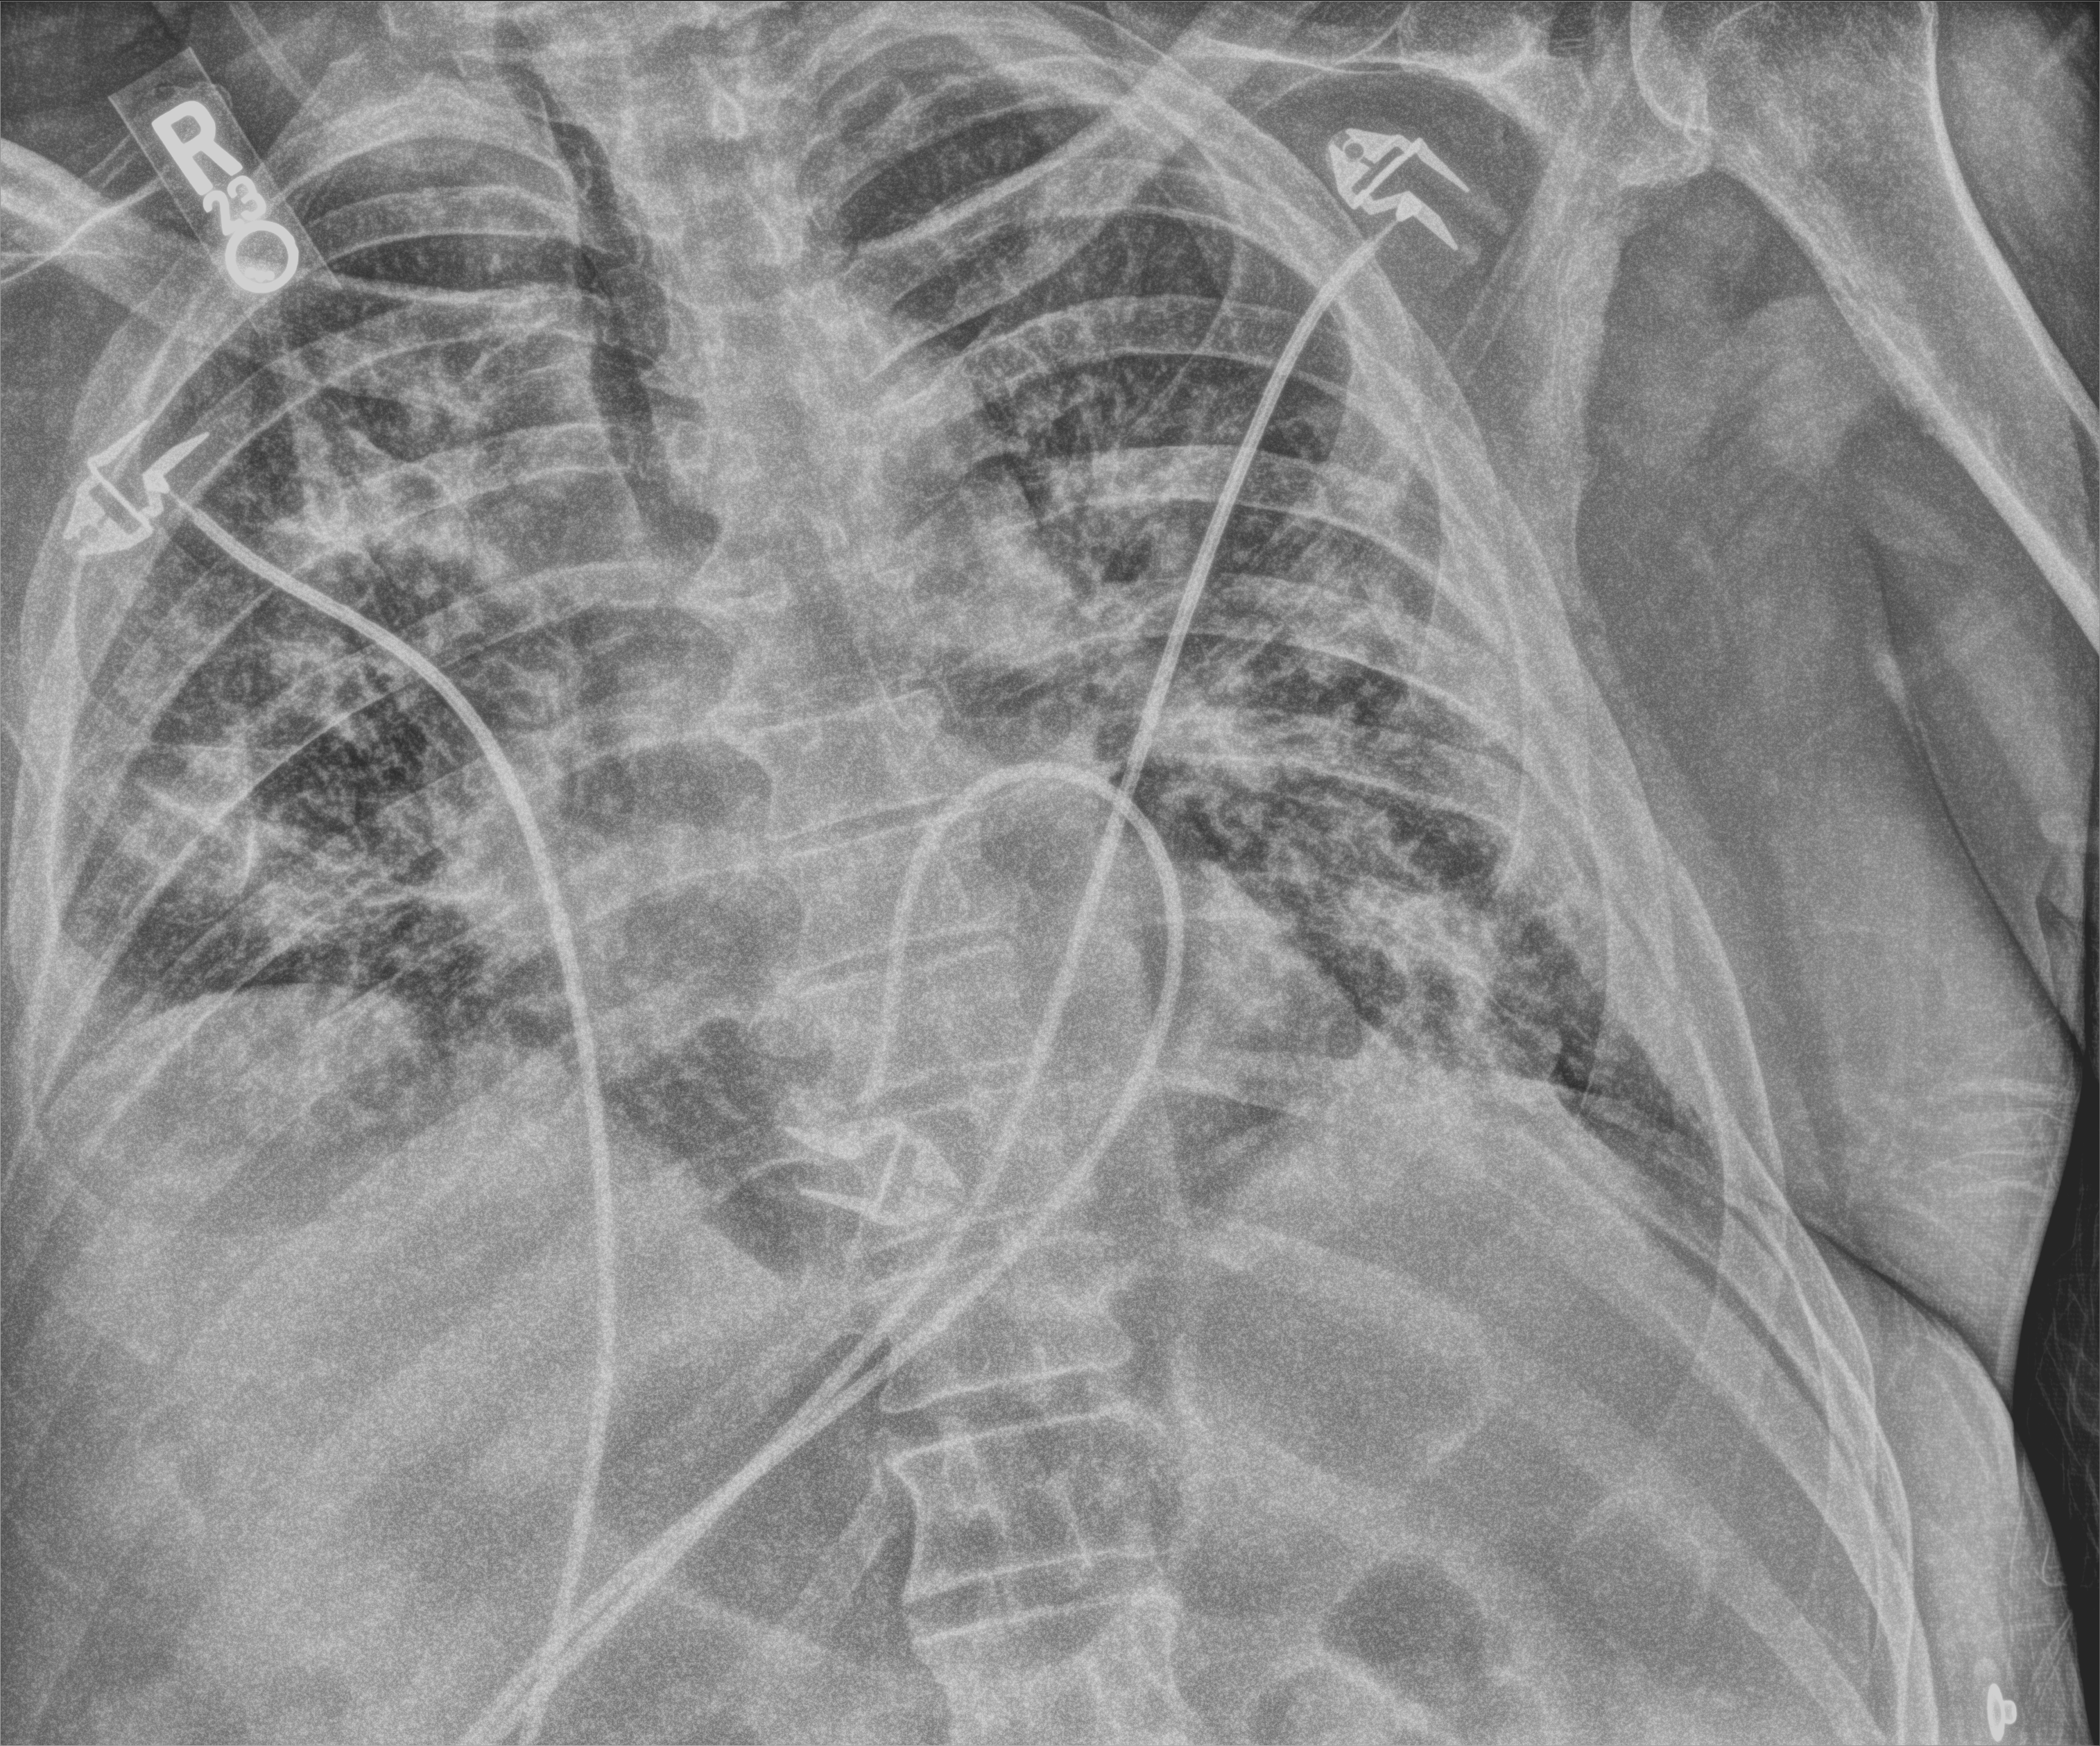
Portable chest radiograph, anteroposterior (AP) projection. Male patient hospitalised with COVID-19, age 60–74 years.
Hospital-stay facts (about this admission, not read from this image; timing relative to this image not recorded): other chronic lung disease (admission record): no; smoking status (admission record): former.